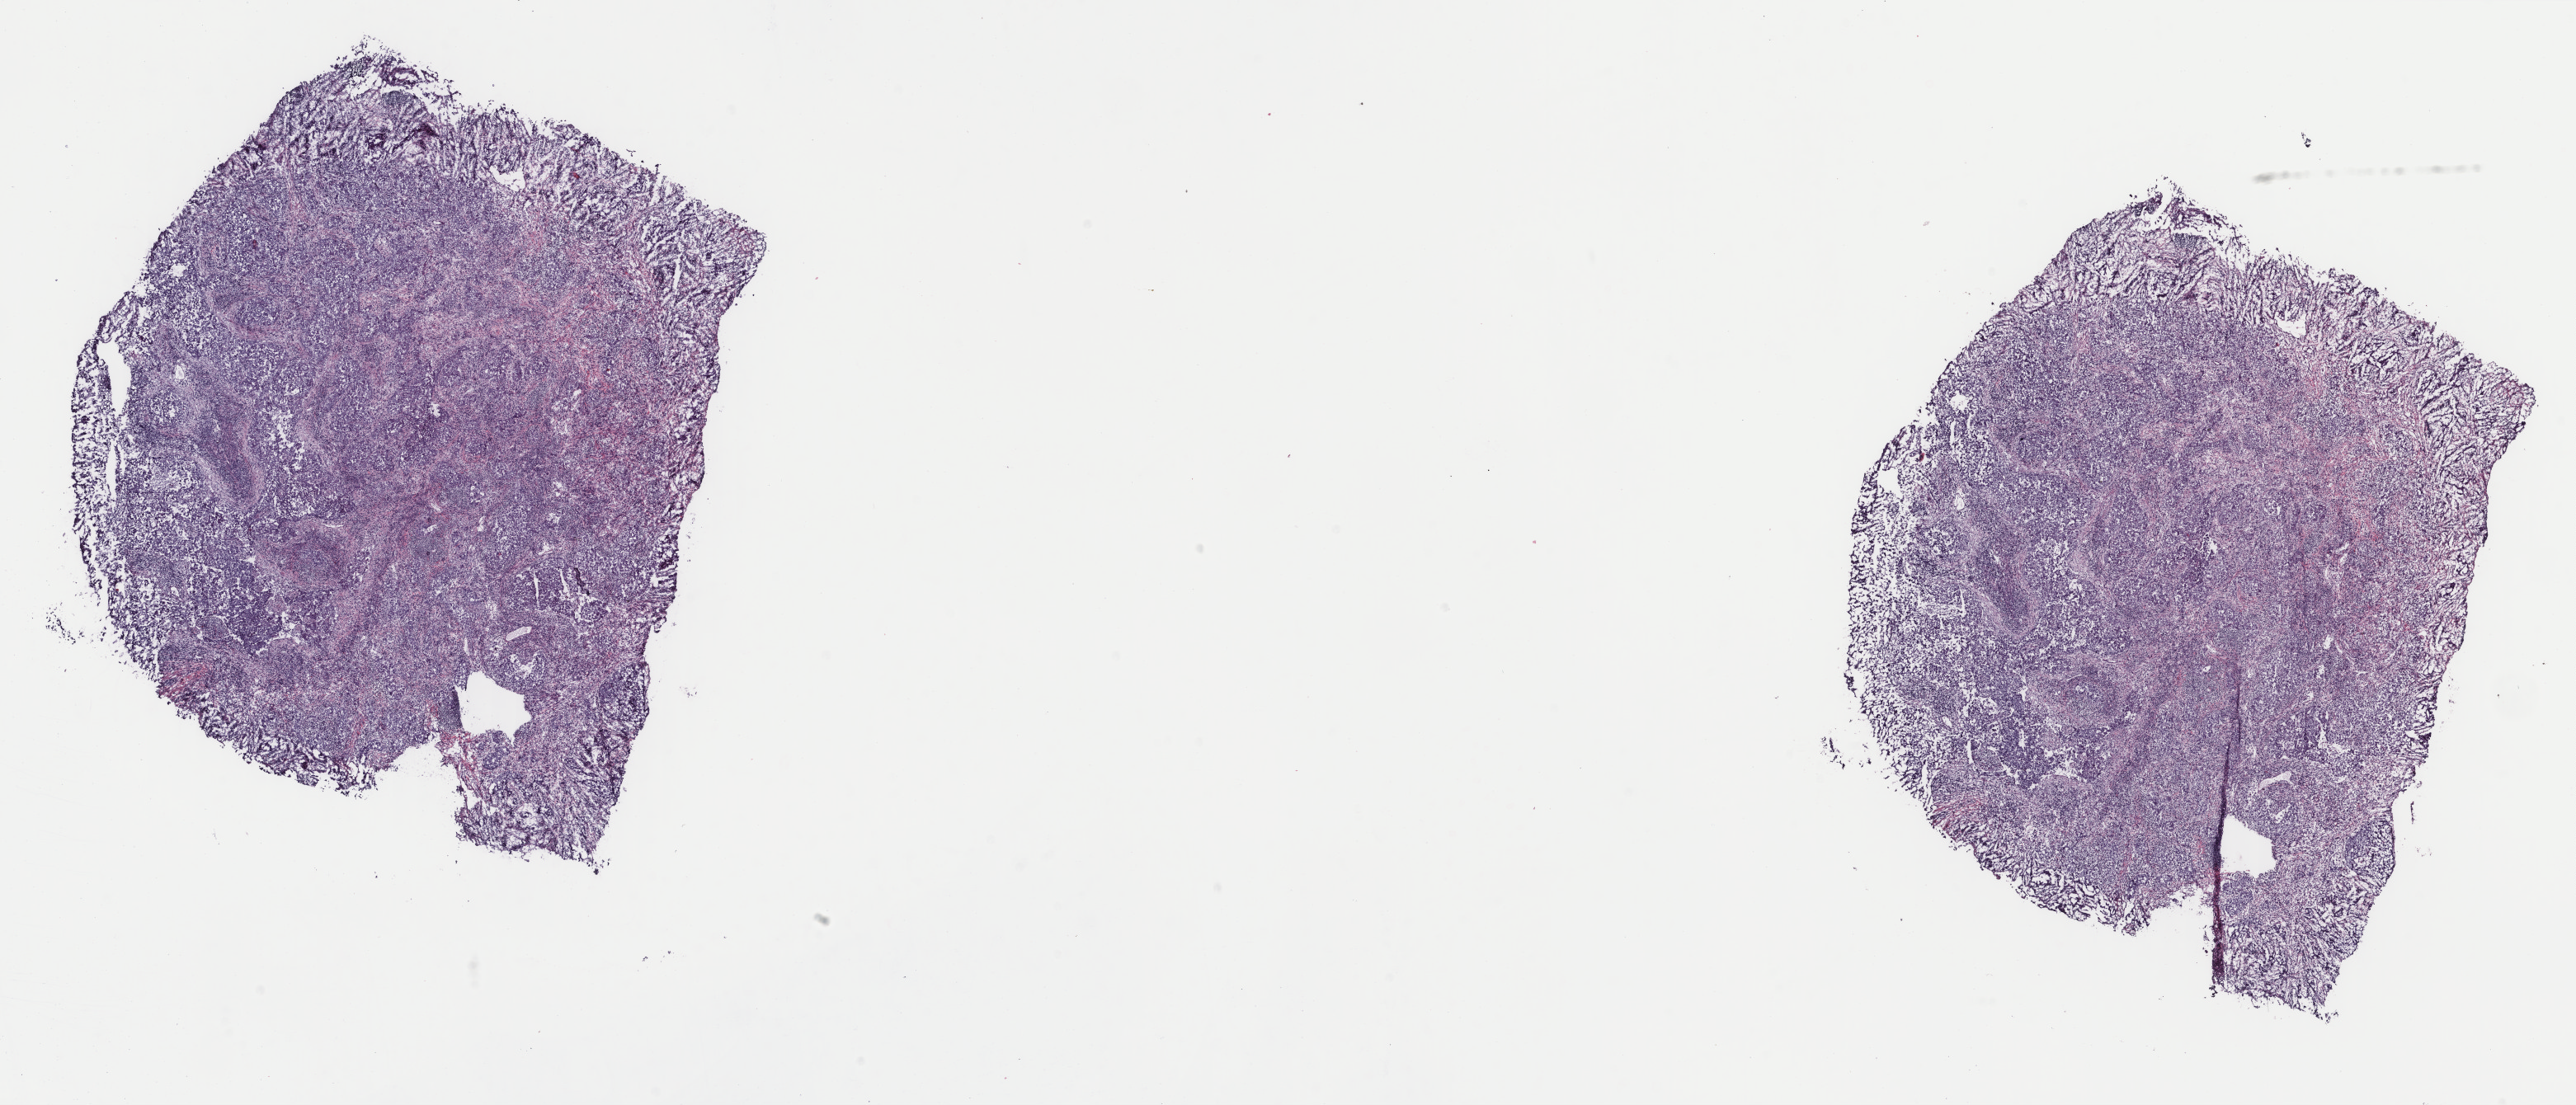
Whole-slide histology image, H&E-stained — whole scanned area (about 24.8 x 10.6 mm, acquisition: 40x scan) shown as a low-resolution overview; frozen section from the top of the tissue portion; lung, primary tumour sample. Patient: female, age at initial diagnosis 73 years.
Histologic diagnosis: Adenocarcinoma, NOS (upper lobe, lung).